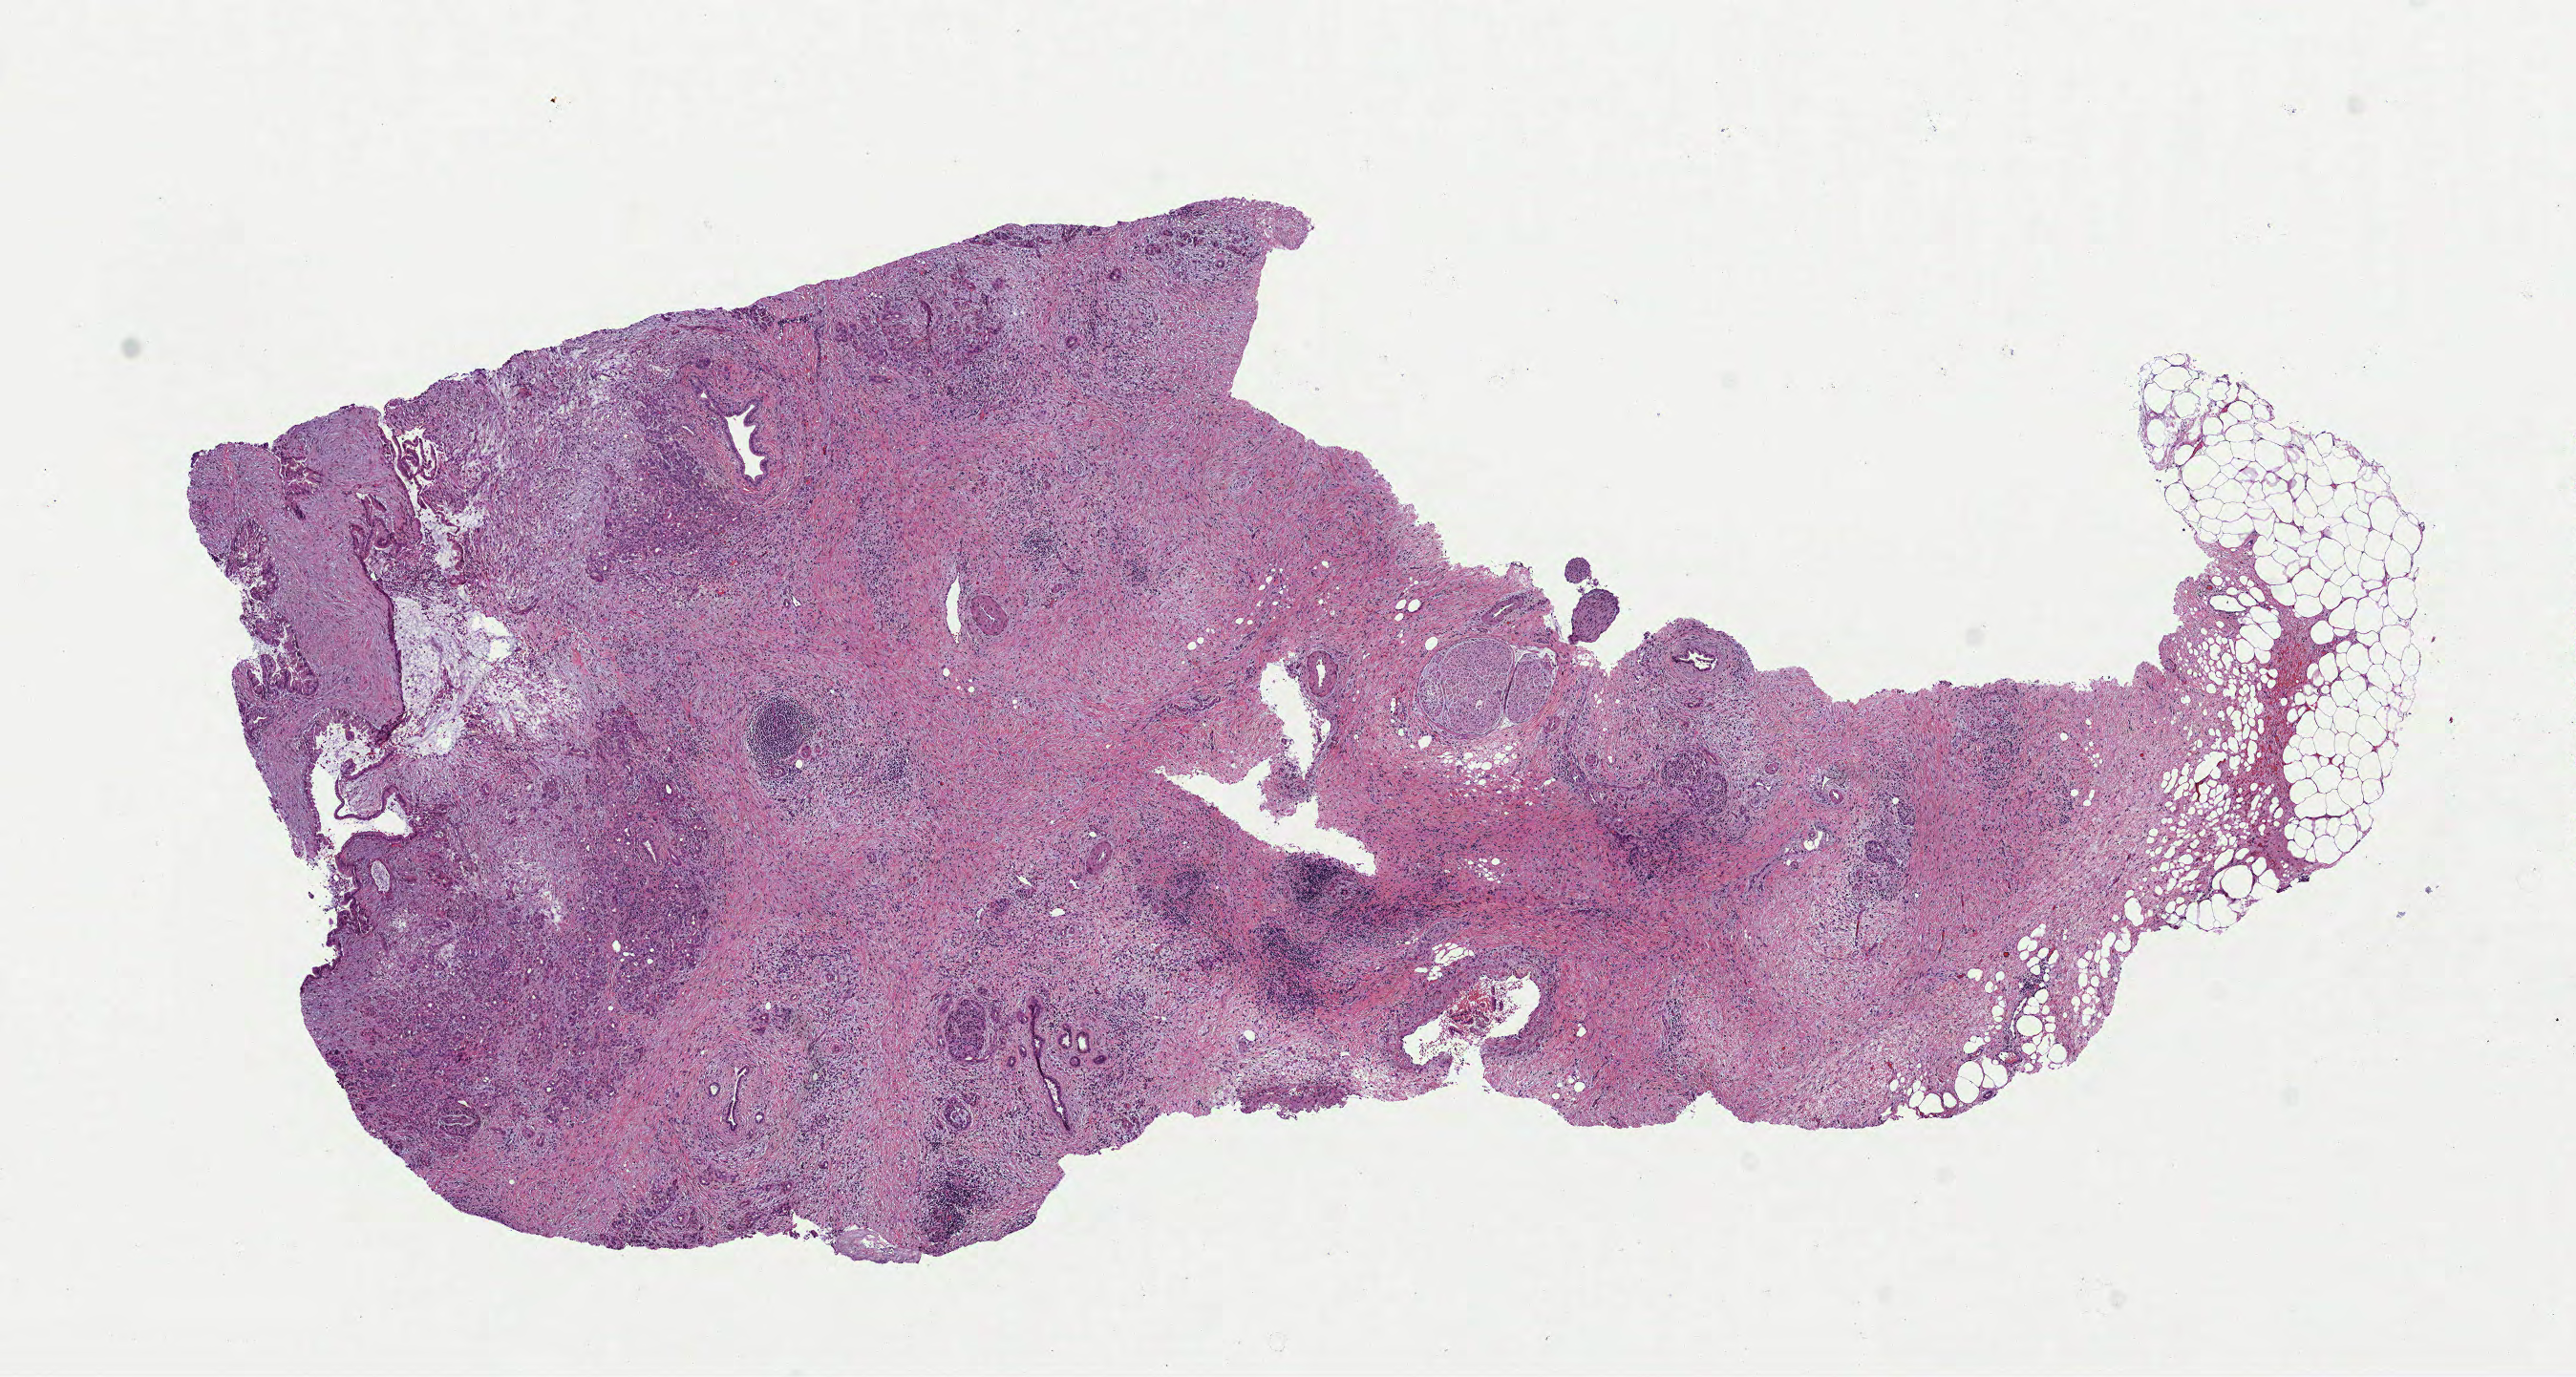
Digitized Hematoxylin and eosin (H&E) stained tissue section (whole slide), a low-resolution overview of the entire scanned area, about 10.9 x 5.8 mm (from a 40x scan); formalin-fixed paraffin-embedded (FFPE) diagnostic section; sample: primary tumour, pancreas. Male patient; age at initial diagnosis 76 years. Histologic grade: G1 (well differentiated).
* TNM: T3 N1 MX
* AJCC pathologic stage: IIB (7th edition)
* histologic diagnosis: Infiltrating duct carcinoma, NOS